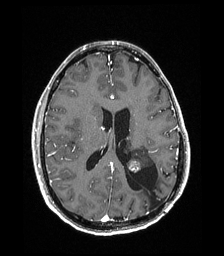
Brain MRI from a brain-tumour surgery series, one axial slice. Position 83 of 192 along the scan axis. T1-weighted post-contrast. 1 mm slice thickness. 224 × 256 image matrix, field of view 224 × 256 mm. From the clinical record (not read from this slice): histopathology: Low grade glioma; IDH mutation: no.
Outlined on this slice (expert manual segmentation):
- previous resection cavity: bounding box (x1, y1, x2, y2) in pixels: (126, 164, 163, 208)
- tumour: (127, 146, 153, 172)